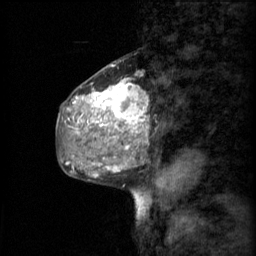
Breast MRI (dynamic contrast-enhanced), one sagittal slice; position 26 of 60 along the scan axis; 3 images stored at this slice position (order not interpretable as contrast timing); 1.5 T; TE 4.2 ms, TR 11 ms; 2 mm slice thickness; 256 × 256 image matrix, field of view 200 × 200 mm. Female patient, age 48 years.
Structures marked on this image (semi-automatic segmentation, software-assisted and operator-edited):
- analysis volume of interest (the breast-tissue region the enhancement analysis was run in; not a lesion): bounding box <69,74,149,147> (left, top, right, bottom; pixels)
- tumour enhancement mask (voxels above the 70 % enhancement threshold inside the analysis volume of interest): <73,78,149,147>